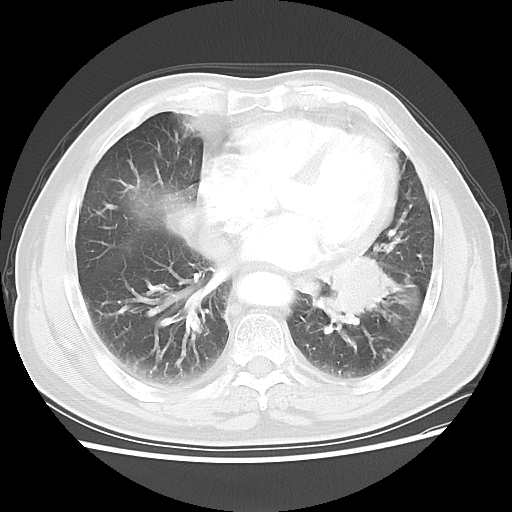
Chest CT, one axial slice; slice 24 of 56 in the series (ordered by position); 120 kVp; lung window (W 1500 / L -600 HU); 5 mm slice thickness; 512 × 512 image matrix, field of view 360 × 360 mm. Male patient, age 75 years. From the clinical record (not read from this slice): clinical TNM (as recorded): T3 N0 M0.
Annotated regions visible in this slice (bounding box drawn by a radiologist):
- lung tumour (recorded histology: squamous cell carcinoma): bounding box <321,242,396,326> (left, top, right, bottom; pixels)